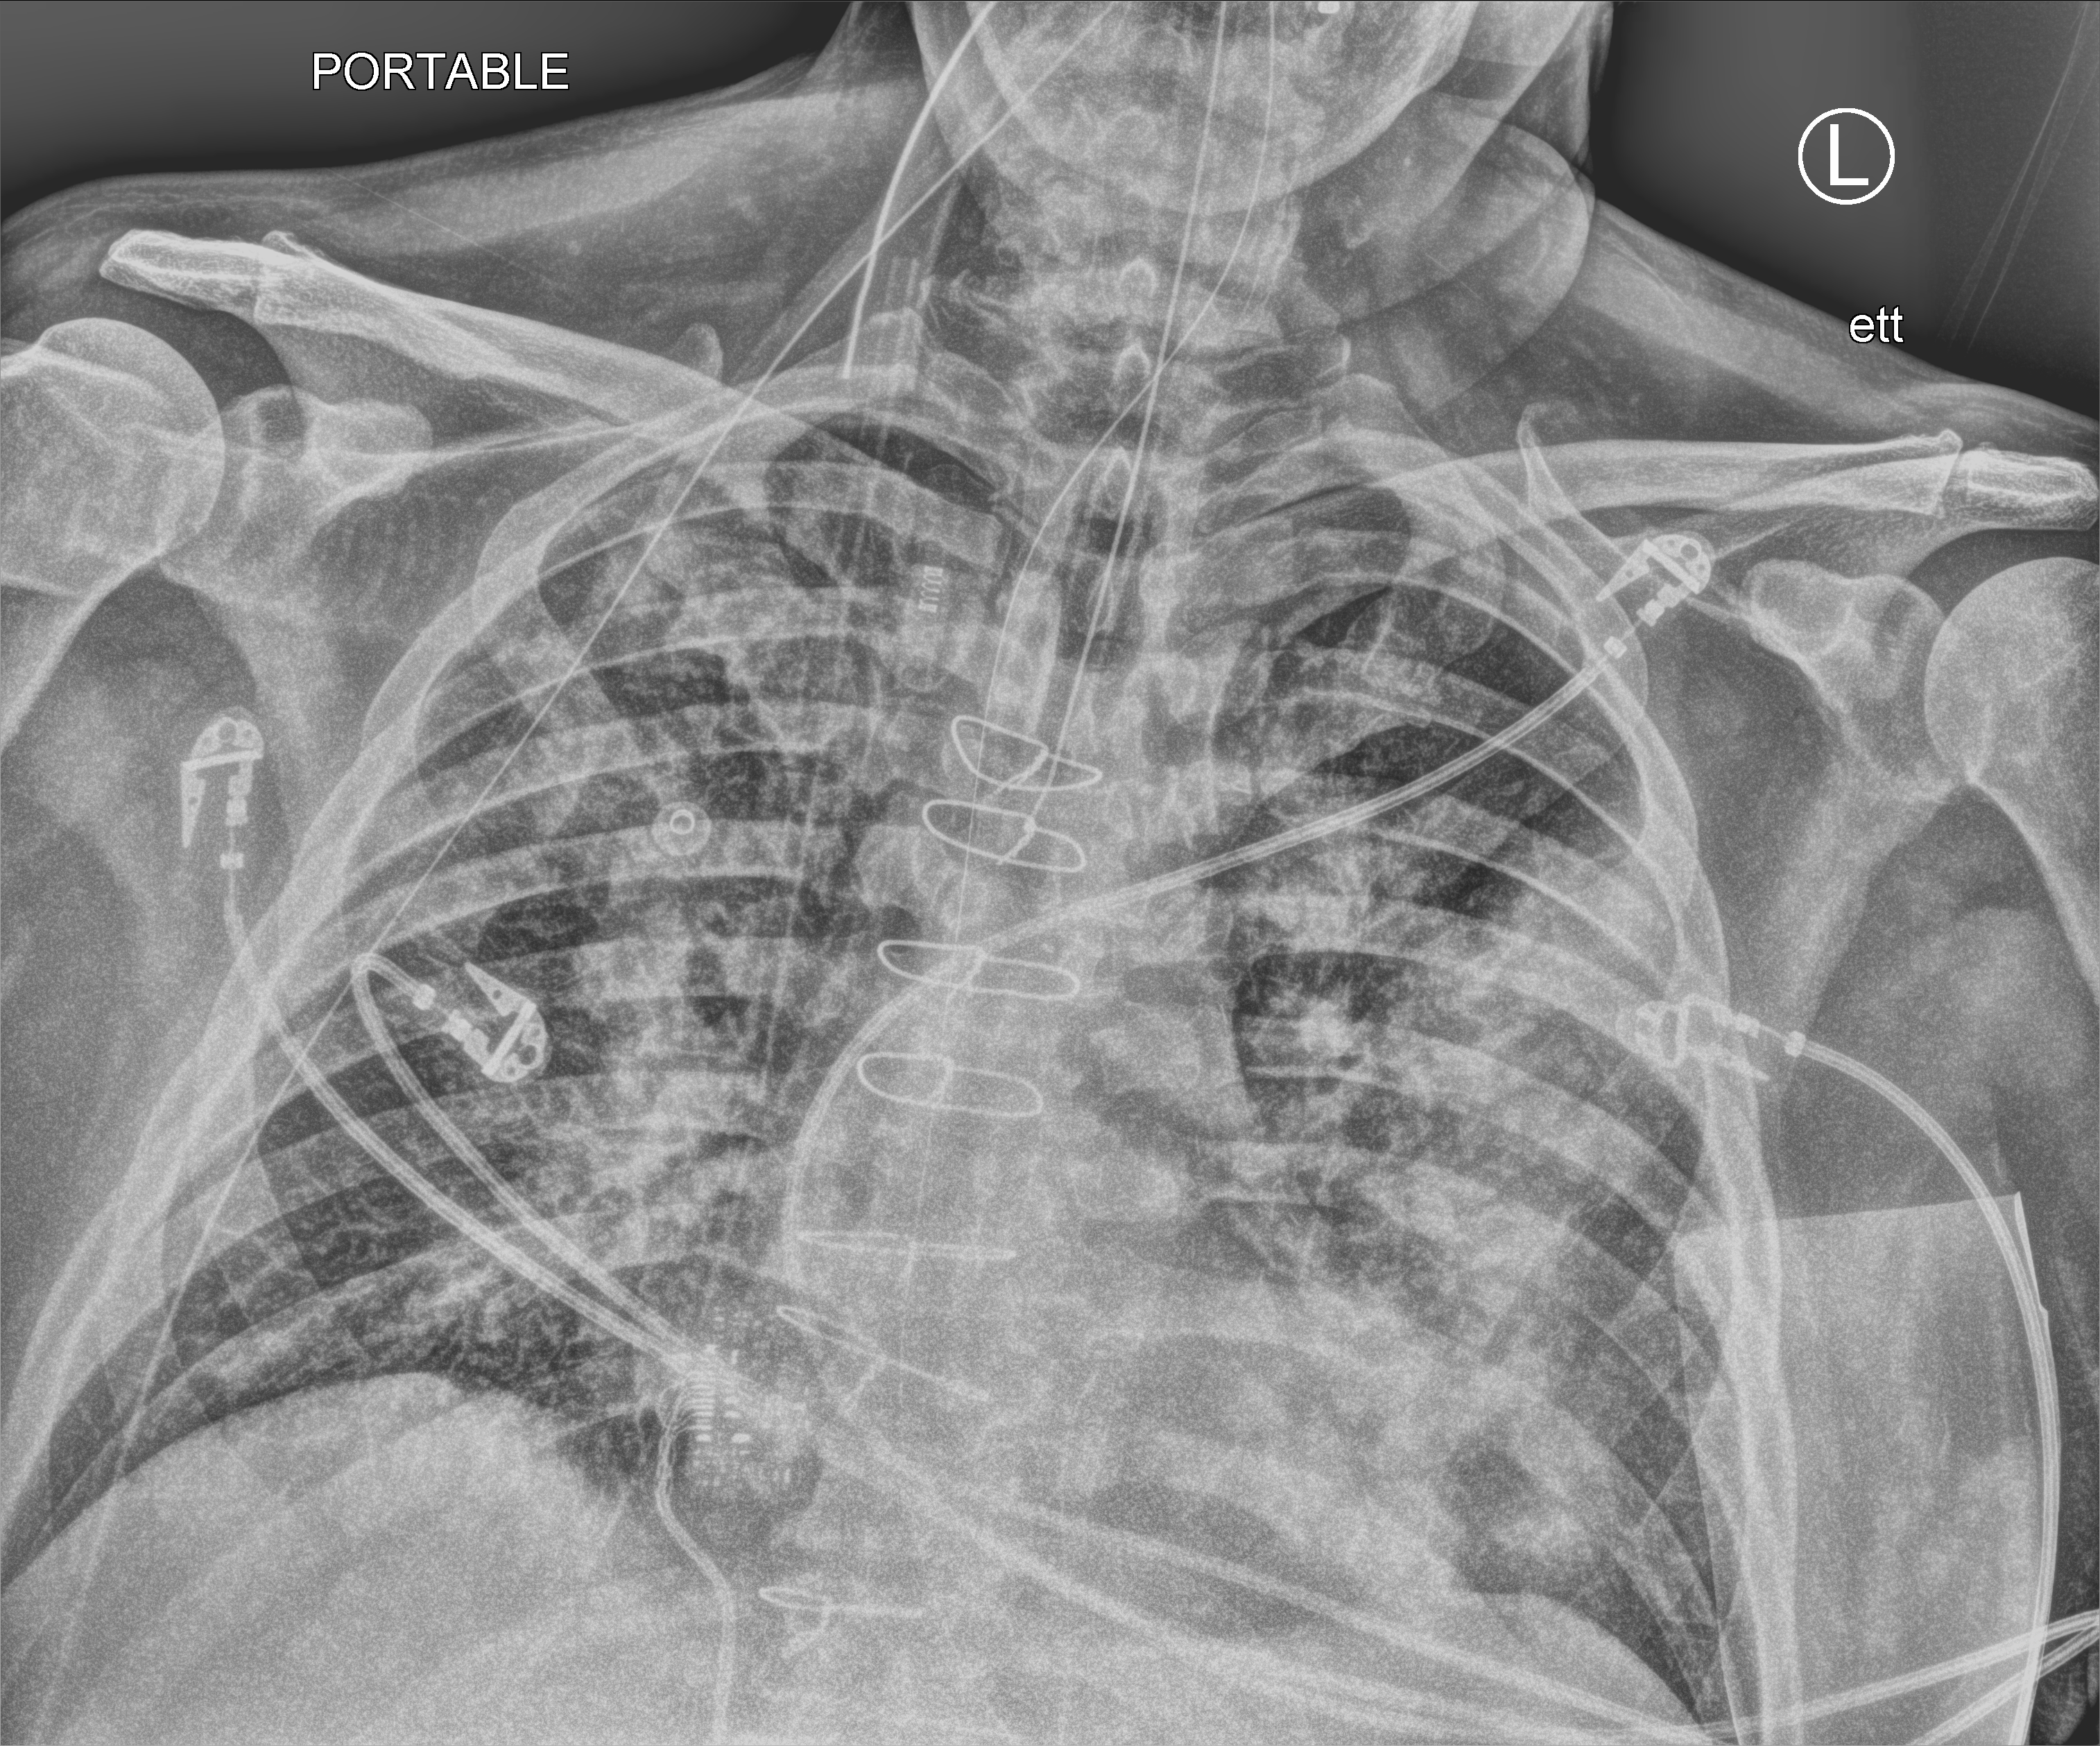
Chest X-ray (portable). Patient hospitalised with COVID-19; male, aged 60–74 years.
Admission-level facts for this patient (not findings on this image; timing relative to this image not recorded):
- admitted to intensive care during this hospital stay: yes